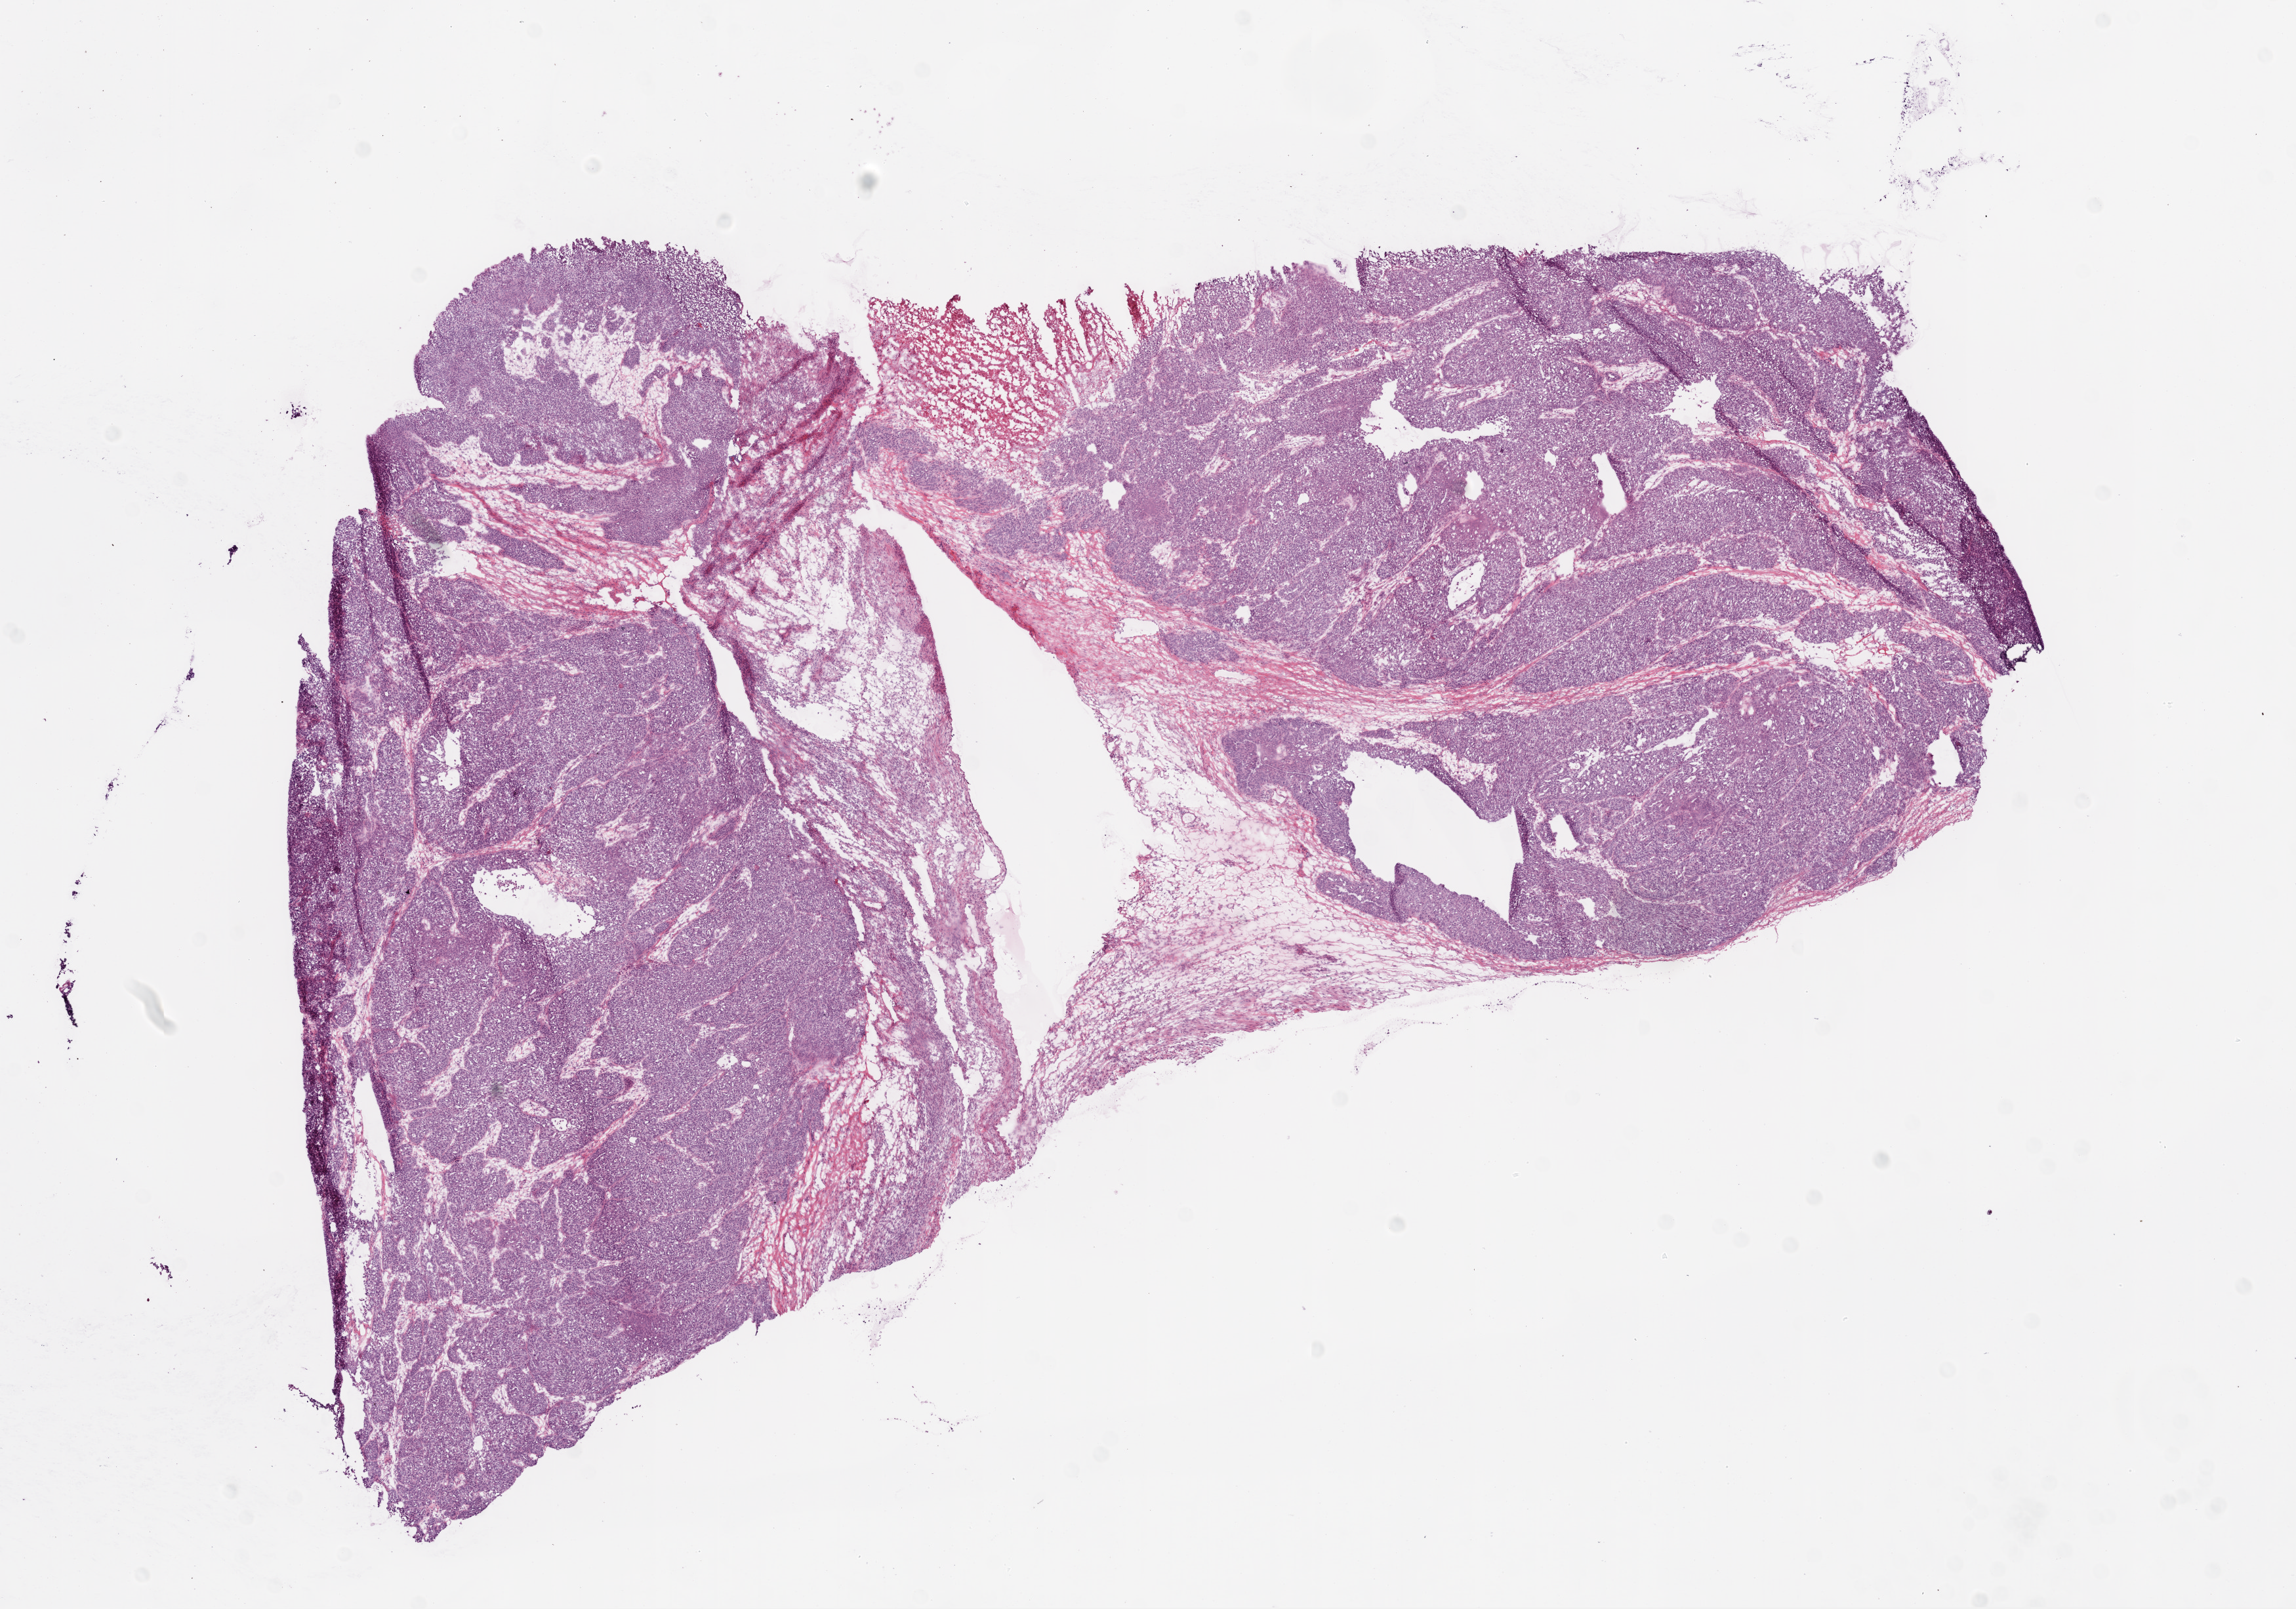
Digitized H&E-stained tissue section (whole slide) — low-resolution overview of the scanned area, about 14.0 x 9.8 mm; frozen section from the top of the tissue portion; primary tumour sample from the ovary. Patient: female, age at initial diagnosis 45 years. Histologic grade: G3 (poorly differentiated). Composition of this section per pathologist review: tumour cells 80%, tumour nuclei 90%, normal cells 0%, stromal cells 10%, necrosis 10%.
FIGO stage: IV. Laterality: bilateral. Pathologic diagnosis: Serous cystadenocarcinoma, NOS.